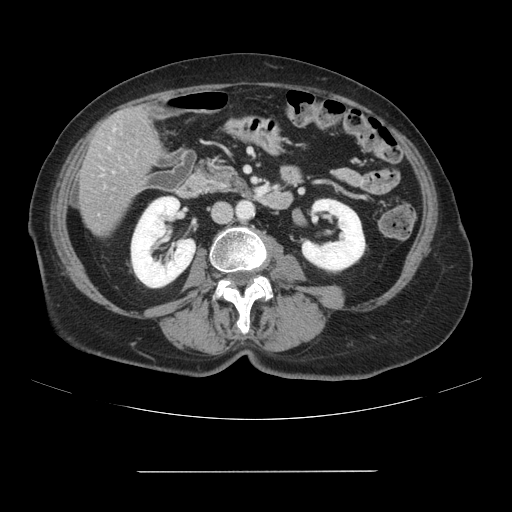
Contrast-enhanced abdominal CT, one axial slice; slice 19 of 111 in the series (ordered by position); 120 kVp; soft-tissue window (W 400 / L 40 HU); 512 × 512 image matrix, field of view 400 × 400 mm. Female patient, age 74 years. From the clinical record (not read from this slice): diagnosis: colorectal cancer liver metastases, imaged before liver resection; multiple liver metastases: yes; largest metastasis: 1.1 cm; chemotherapy before resection: yes.
Annotated regions visible in this slice (expert manual segmentation):
- liver: bounding box <79,105,163,237> (left, top, right, bottom; pixels)